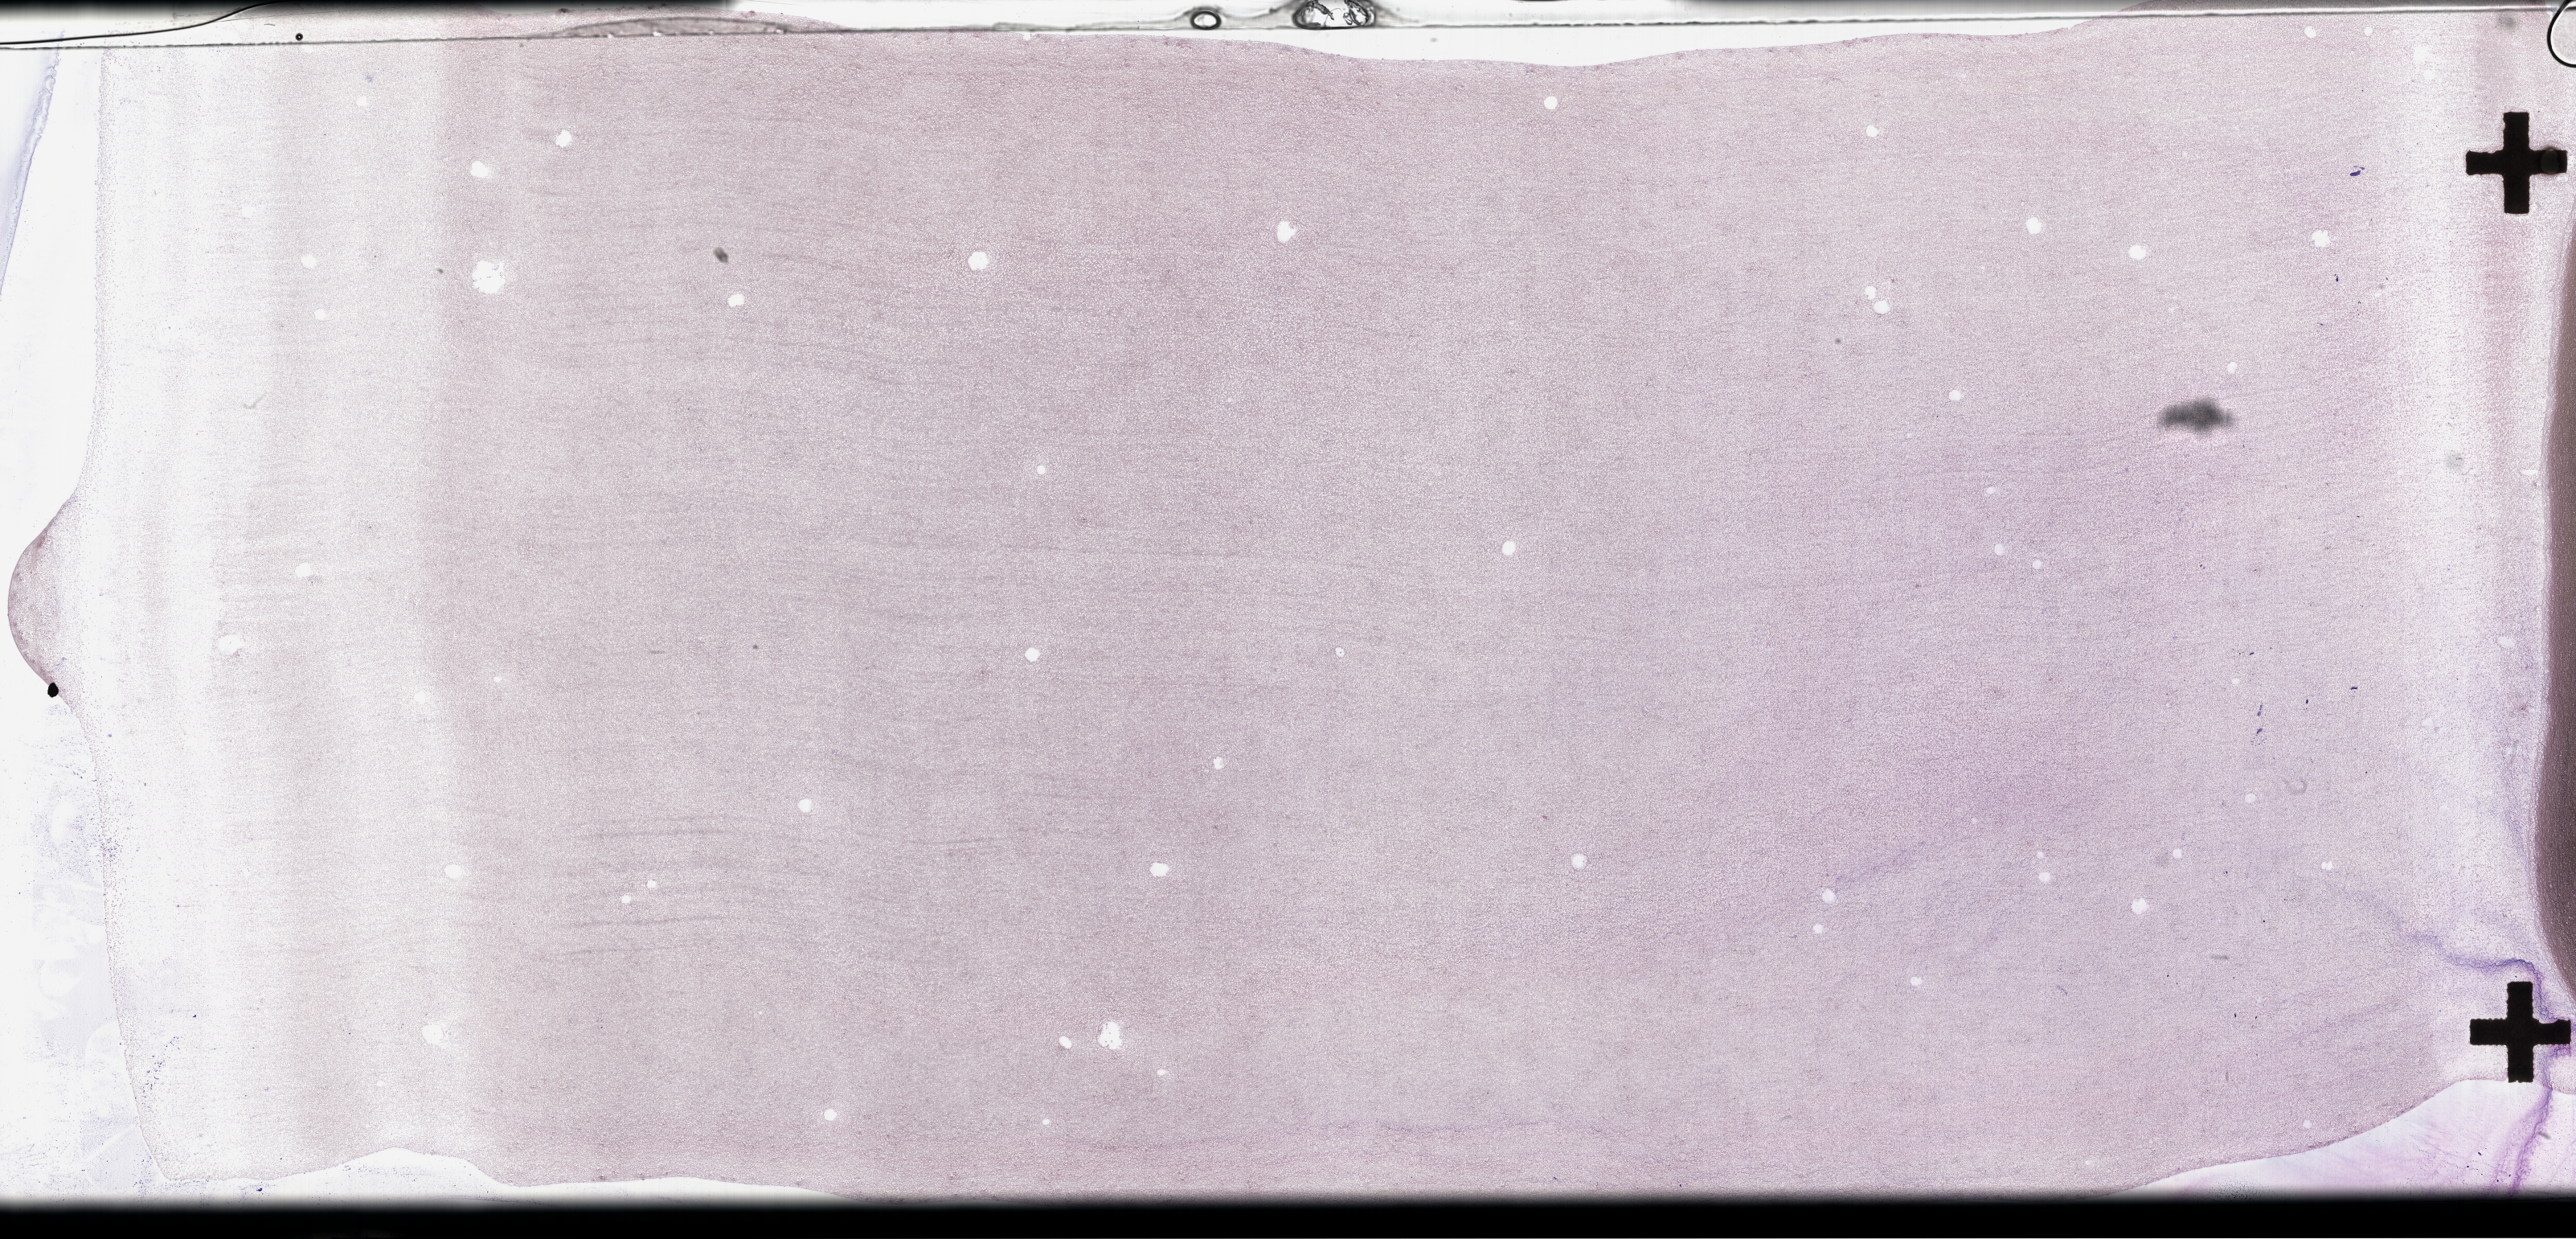
Wright–Giemsa-stained bone marrow smear, whole-slide image, a low-resolution overview of the entire scanned area, about 51.8 x 24.9 mm, smear from an EDTA sample, collected at disease progression. Male patient.
From a patient with: Plasma Cell Myeloma.